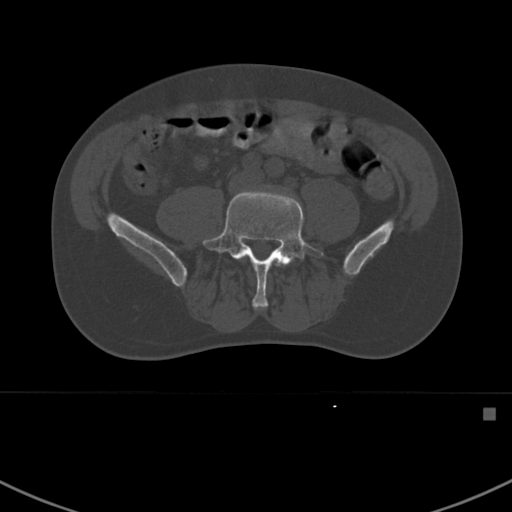
CT including the spine, one axial slice. Position 224 of 412 along the scan axis. Bone window (W 1800 / L 400 HU). 1.5 mm slice thickness. 512 × 512 image matrix. Male patient, age 59 years. Case-level facts recorded for this patient, not image findings: primary cancer: prostate.
Outlined on this slice (semi-automatically segmented with operator editing):
- L4 vertebra: box from (x=276, y=262) to (x=288, y=266) px
- L5 vertebra: (x=202, y=190)–(x=324, y=309)